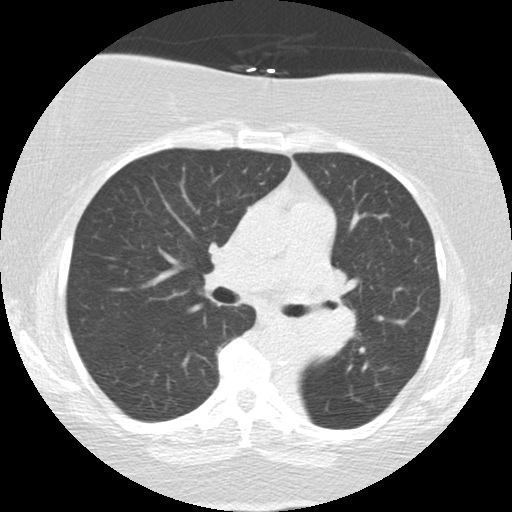
Low-dose screening chest CT, one axial slice. Position 80 of 136 along the scan axis. Lung window (W 1500 / L -600 HU). 2.5 mm slice thickness. 512 × 512 image matrix, field of view 309 × 309 mm.
Annotated regions visible in this slice (expert manual segmentation):
- lesion 2 (tumor, mediastinum): bounding box (x1, y1, x2, y2) in pixels: (297, 268, 358, 357)